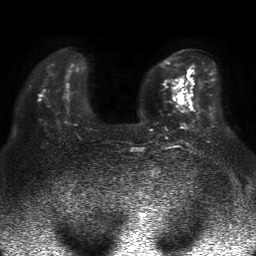
Breast MRI, one axial slice; position 12 of 50 along the scan axis; diffusion-weighted series; image 2 of 4 stored at this slice position (different b-values; order by instance number); 1.5 T; 4 mm slice thickness; 256 × 256 image matrix, field of view 360 × 360 mm. Female patient.
Outlined on this slice (outlined manually by an expert reader):
- tumour on diffusion-weighted imaging: box from (x=179, y=99) to (x=183, y=104) px